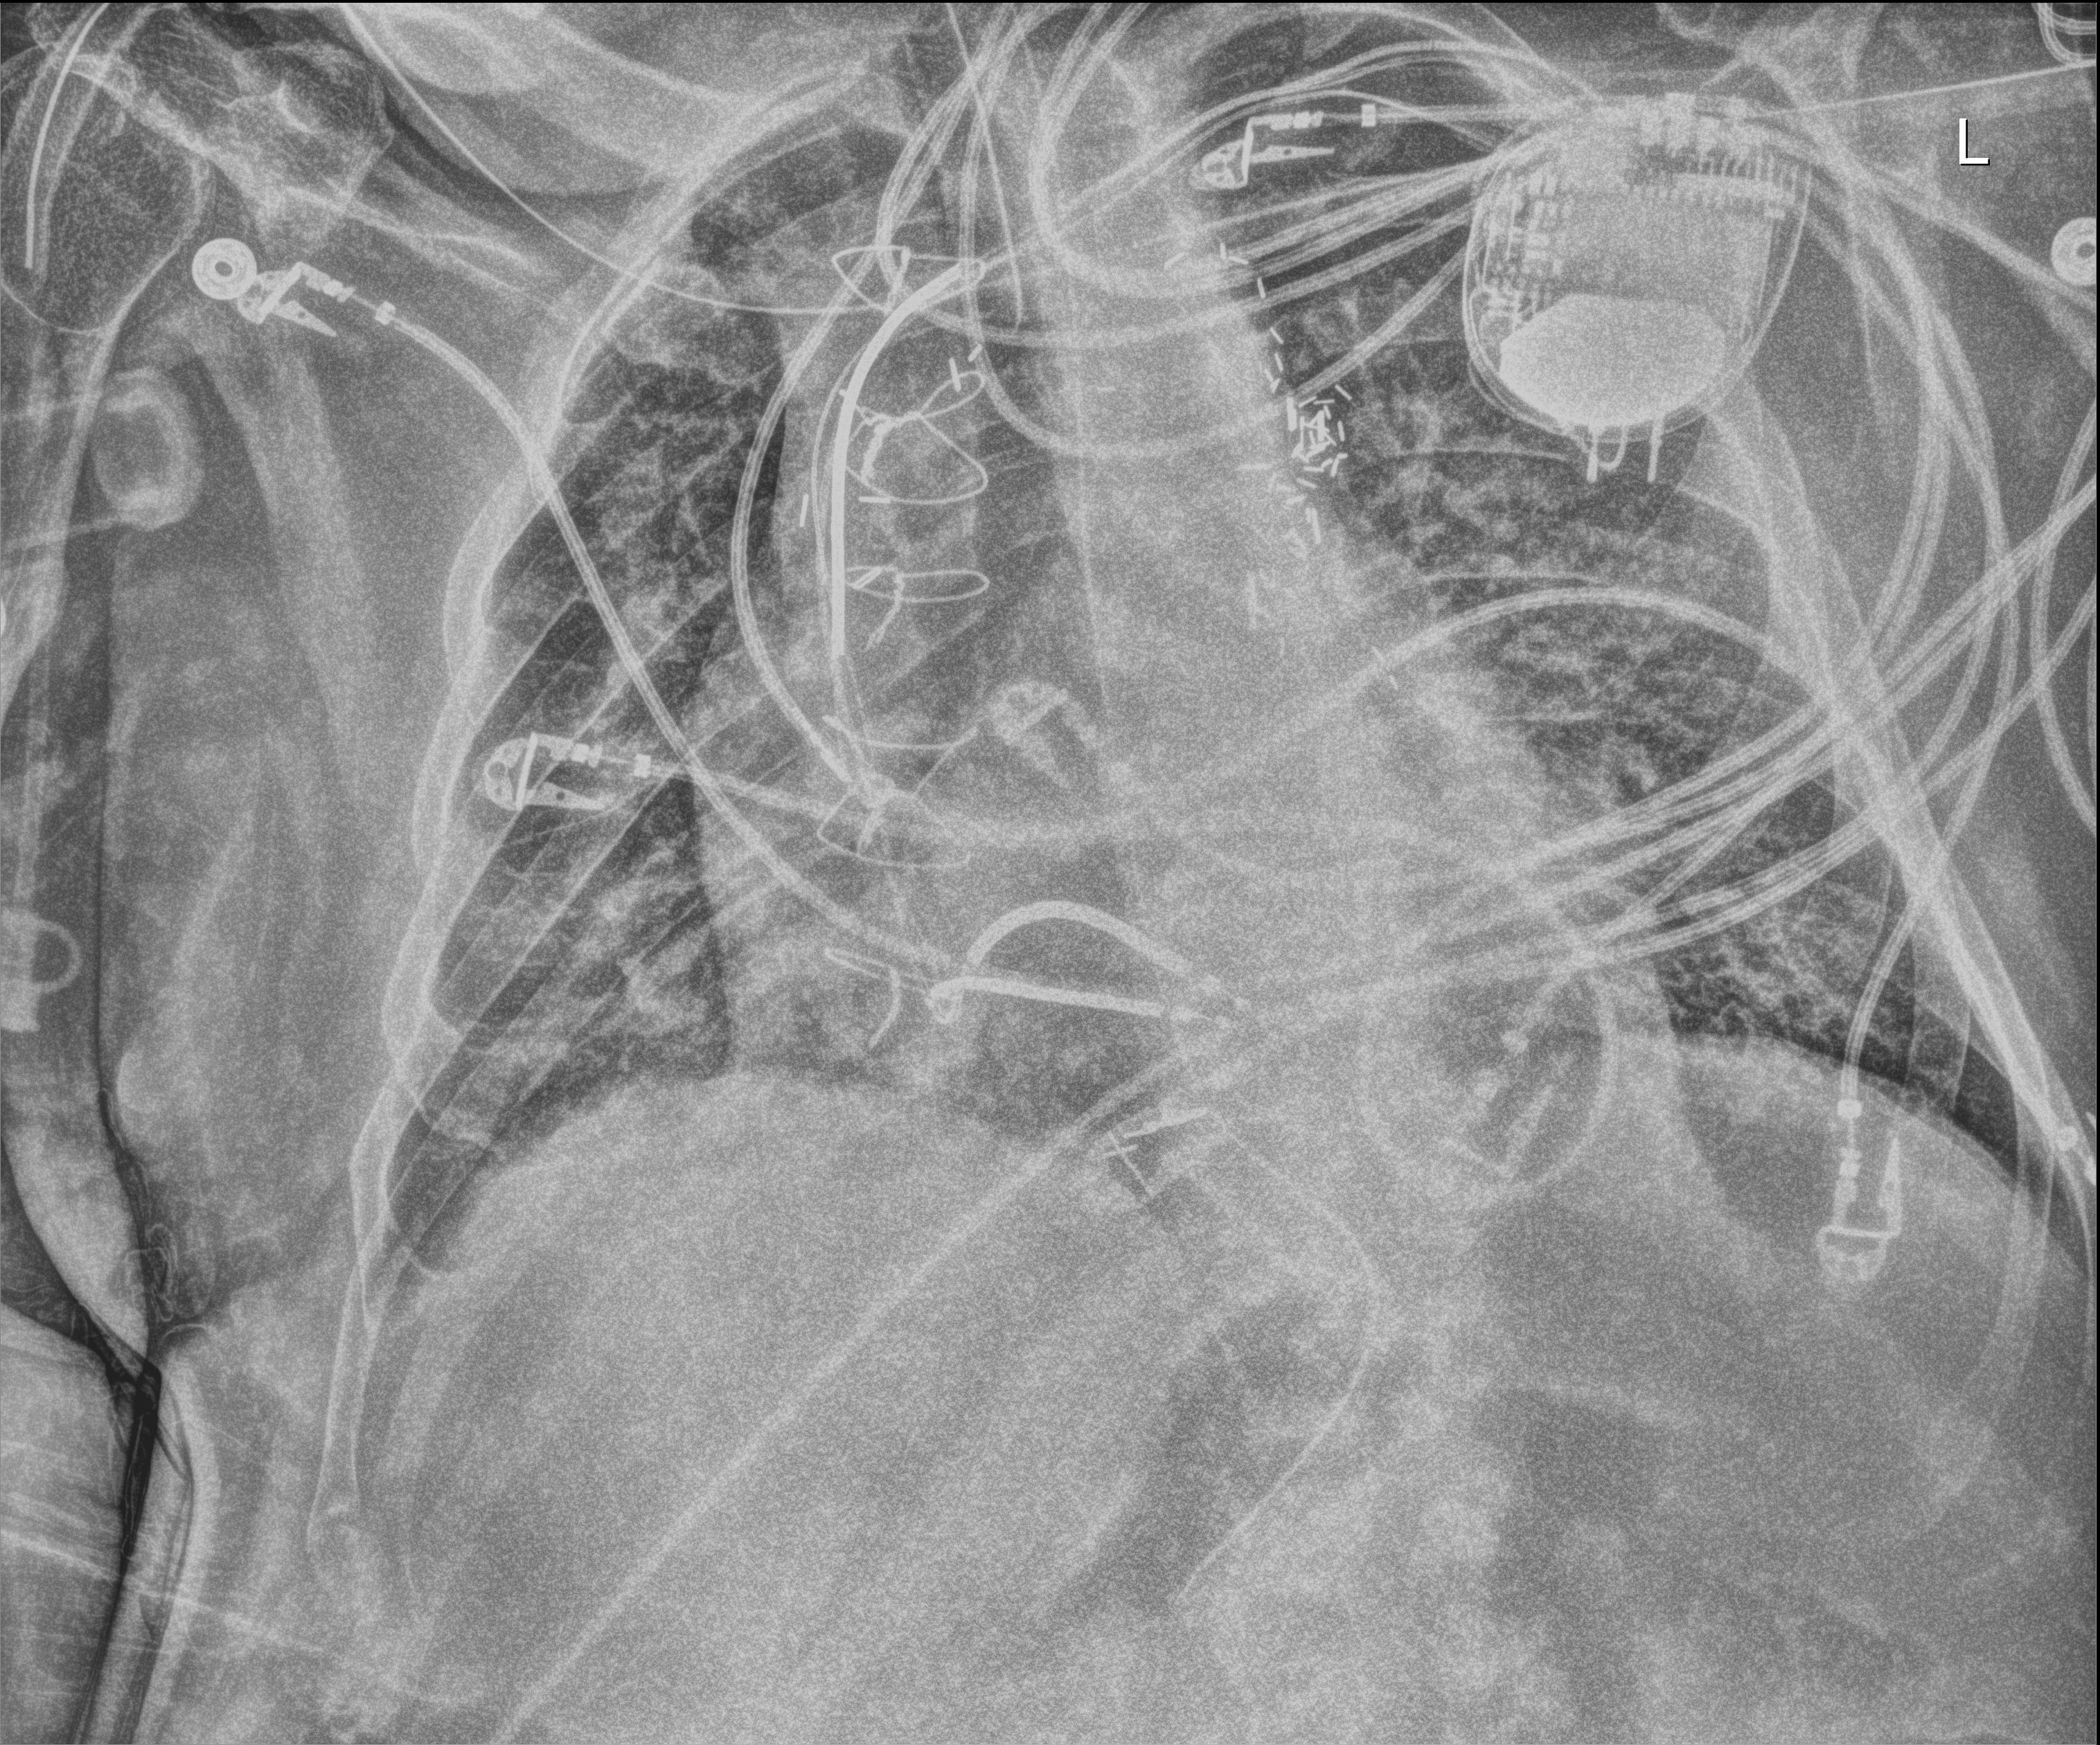
Portable chest radiograph, anteroposterior (AP) projection. Patient hospitalised with COVID-19; male, aged 60–74 years.
Hospital-stay facts (about this admission, not read from this image; timing relative to this image not recorded): hypertension (admission record): yes.